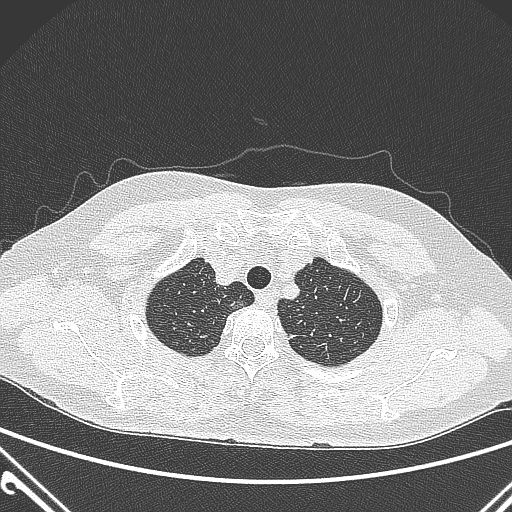
Chest CT, one axial slice; position 247 of 300 along the scan axis; 120 kVp; lung window (W 1500 / L -600 HU); 1 mm slice thickness; 512 × 512 image matrix, field of view 350 × 350 mm. Patient: female, 54 years. From the clinical record (not read from this slice): clinical TNM (as recorded): T1a N0 M0; histopathological grade: G1.
Outlined on this slice (rectangle marked by the reading radiologist):
- lung tumour (recorded histology: adenocarcinoma): bounding box <226,290,250,316> (left, top, right, bottom; pixels)